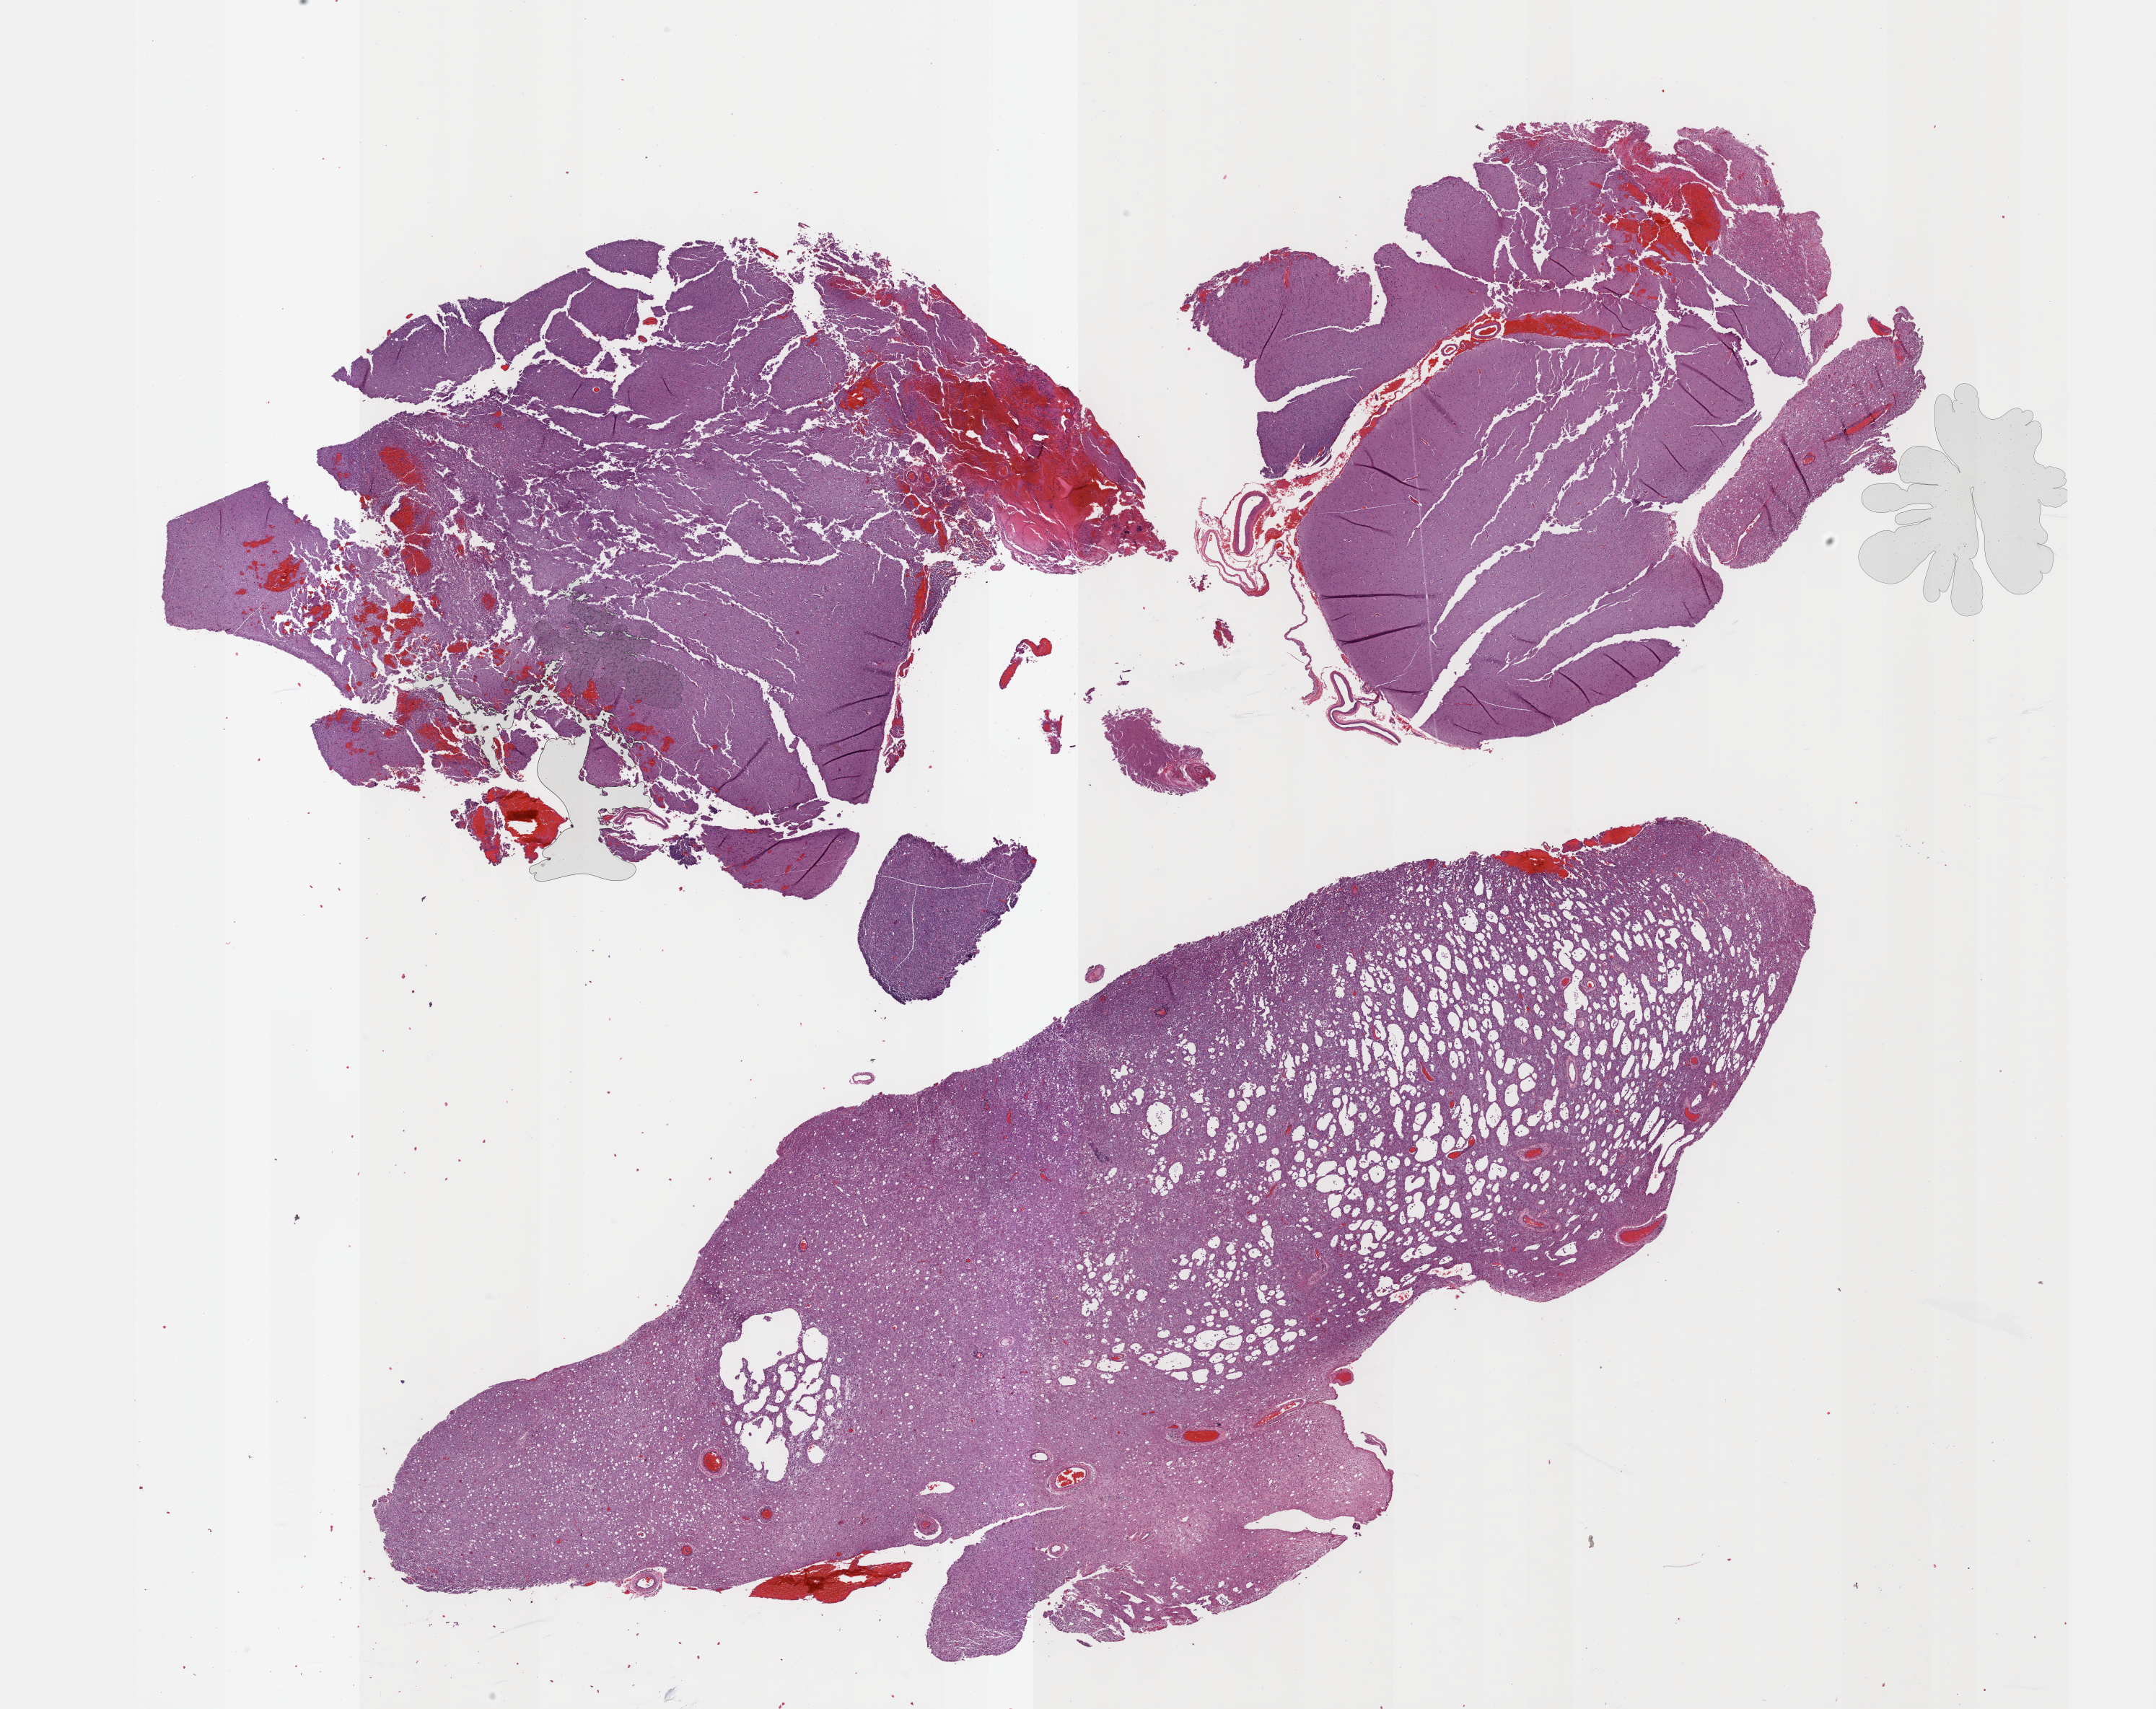
Whole-slide histology image, Hematoxylin and eosin (H&E) stained — shown as a low-resolution overview of the whole scanned area (about 24.1 x 19.1 mm, slide scanned at 40x), formalin-fixed paraffin-embedded (FFPE) diagnostic section, sample: primary tumour, brain. Male patient; age at initial diagnosis 35 years. Histologic grade: G3 (poorly differentiated).
* pathologic diagnosis: Oligodendroglioma, anaplastic